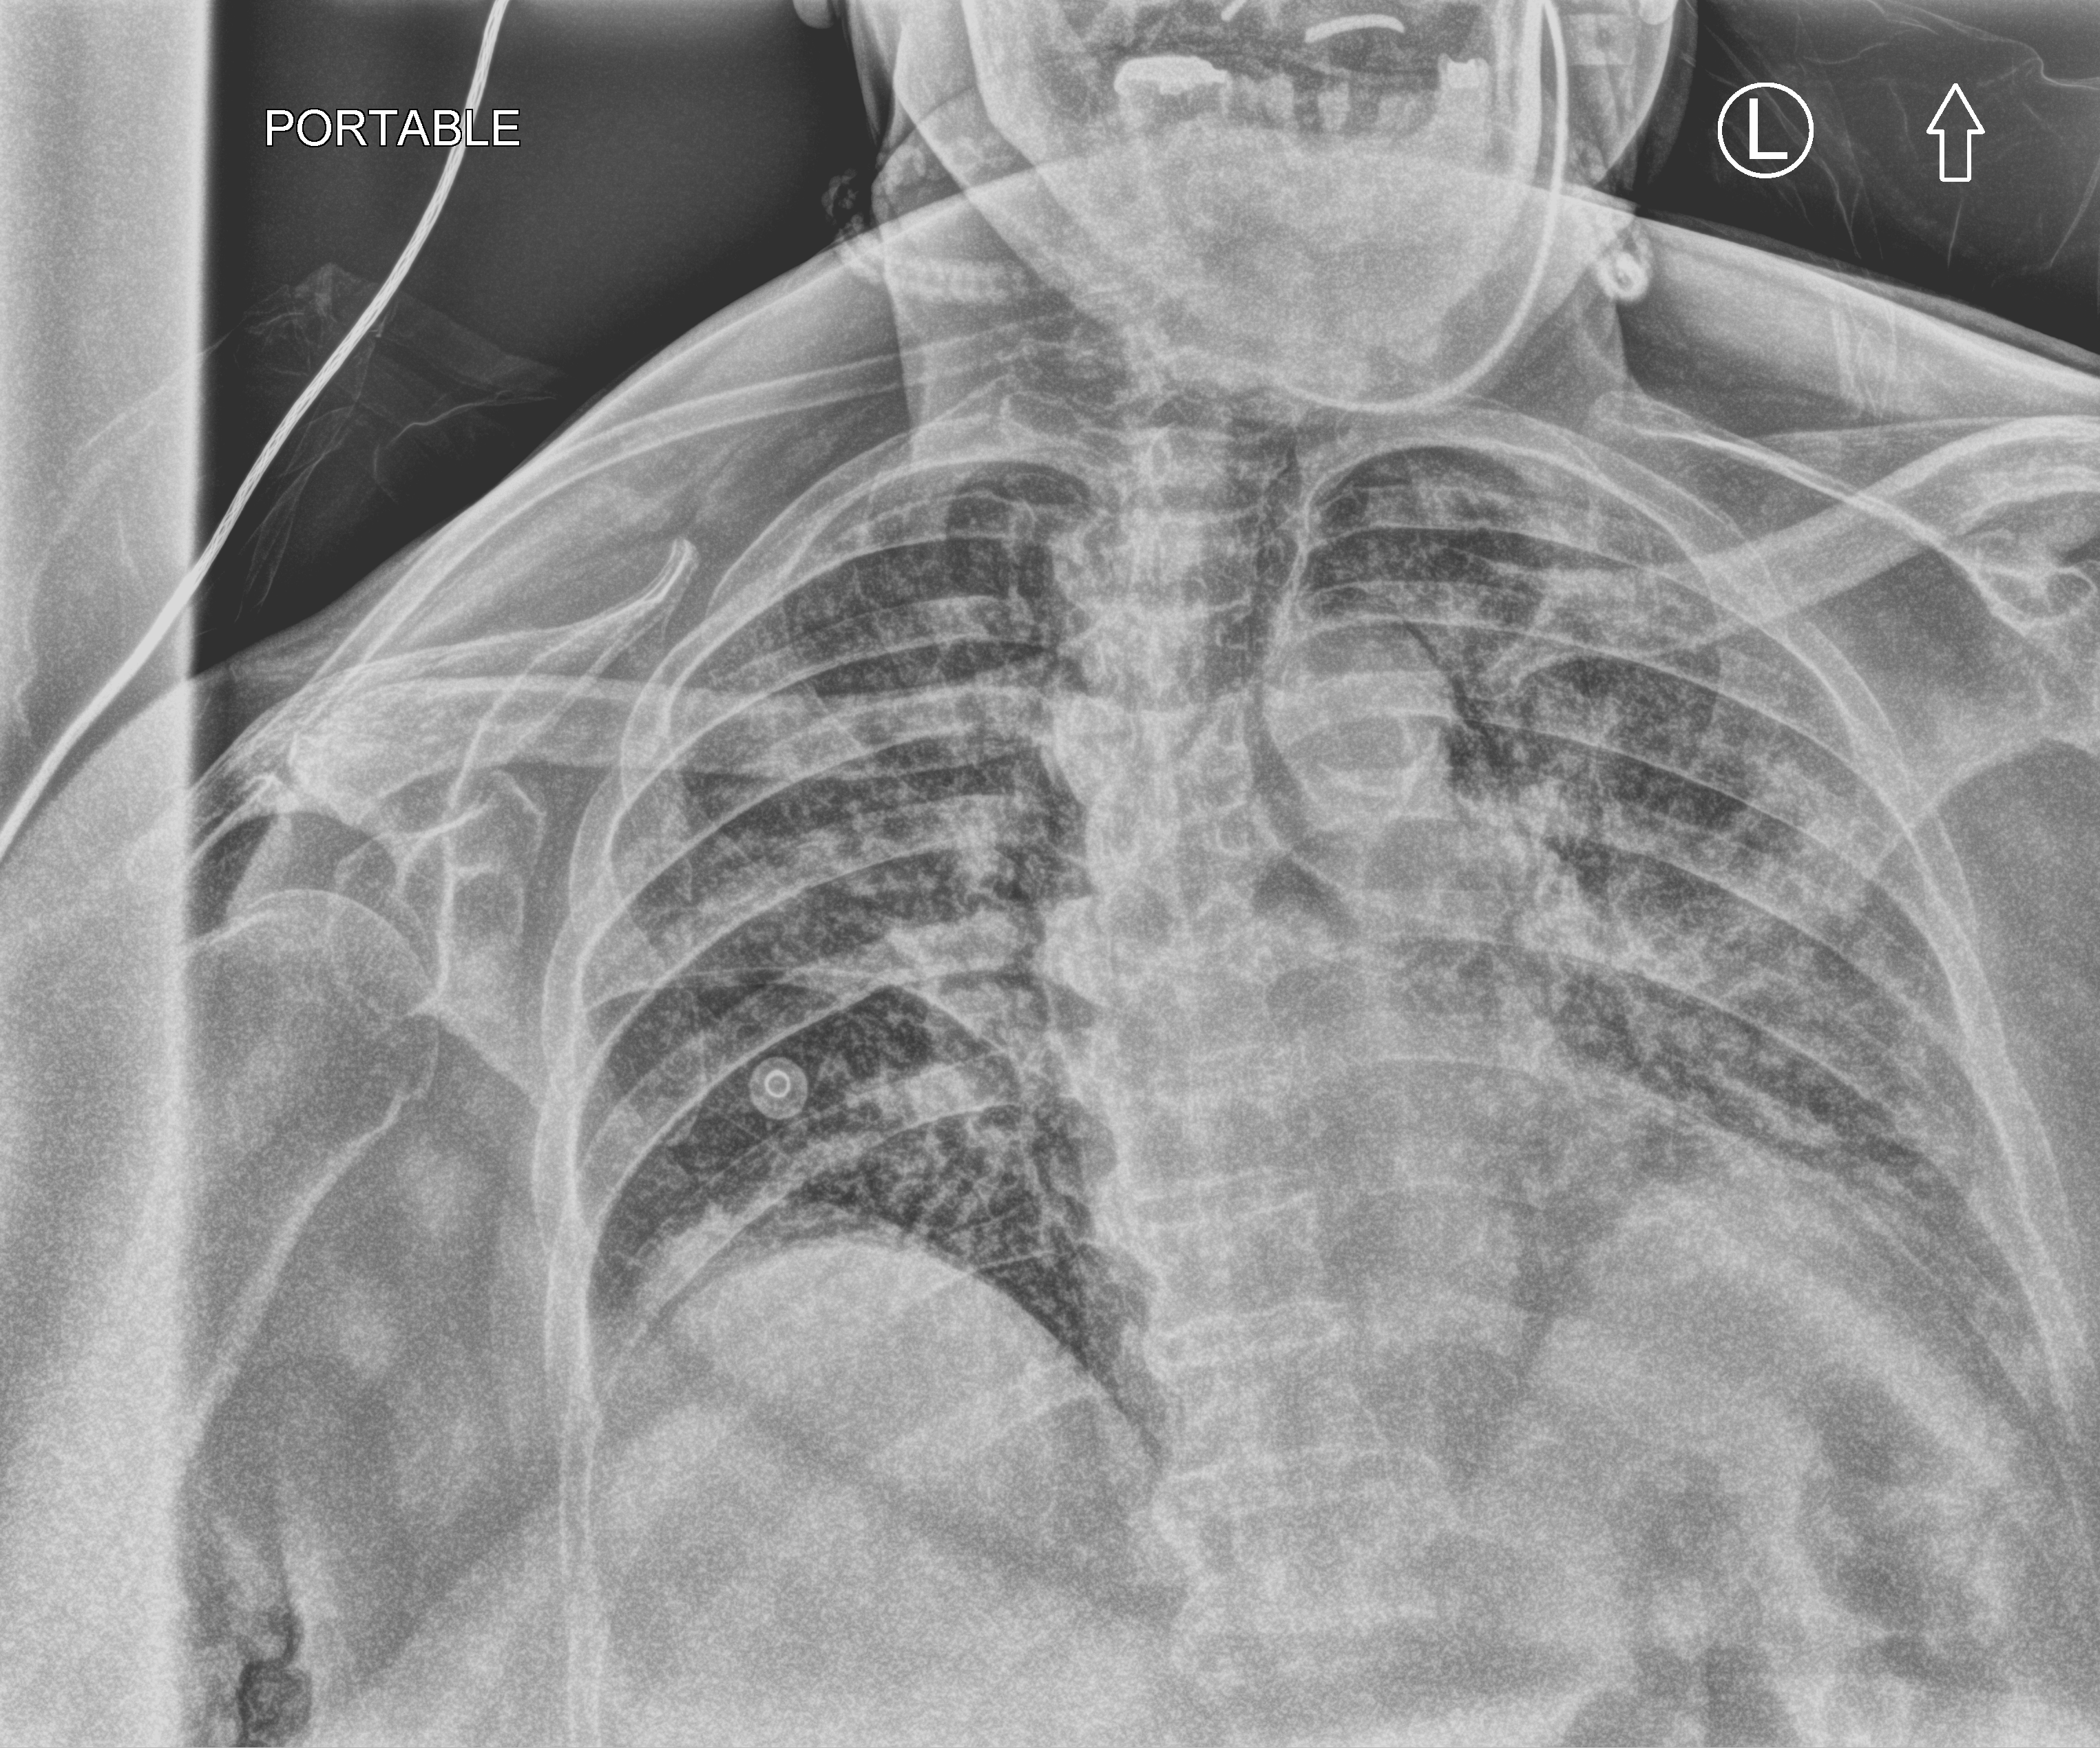
Portable chest radiograph; anteroposterior (AP) projection. Patient hospitalised with COVID-19; female, aged 75–90 years.
Hospital-stay facts (about this admission, not read from this image; timing relative to this image not recorded): admitted to intensive care during this hospital stay: no; hypertension (admission record): yes; mechanically ventilated during this hospital stay: no.